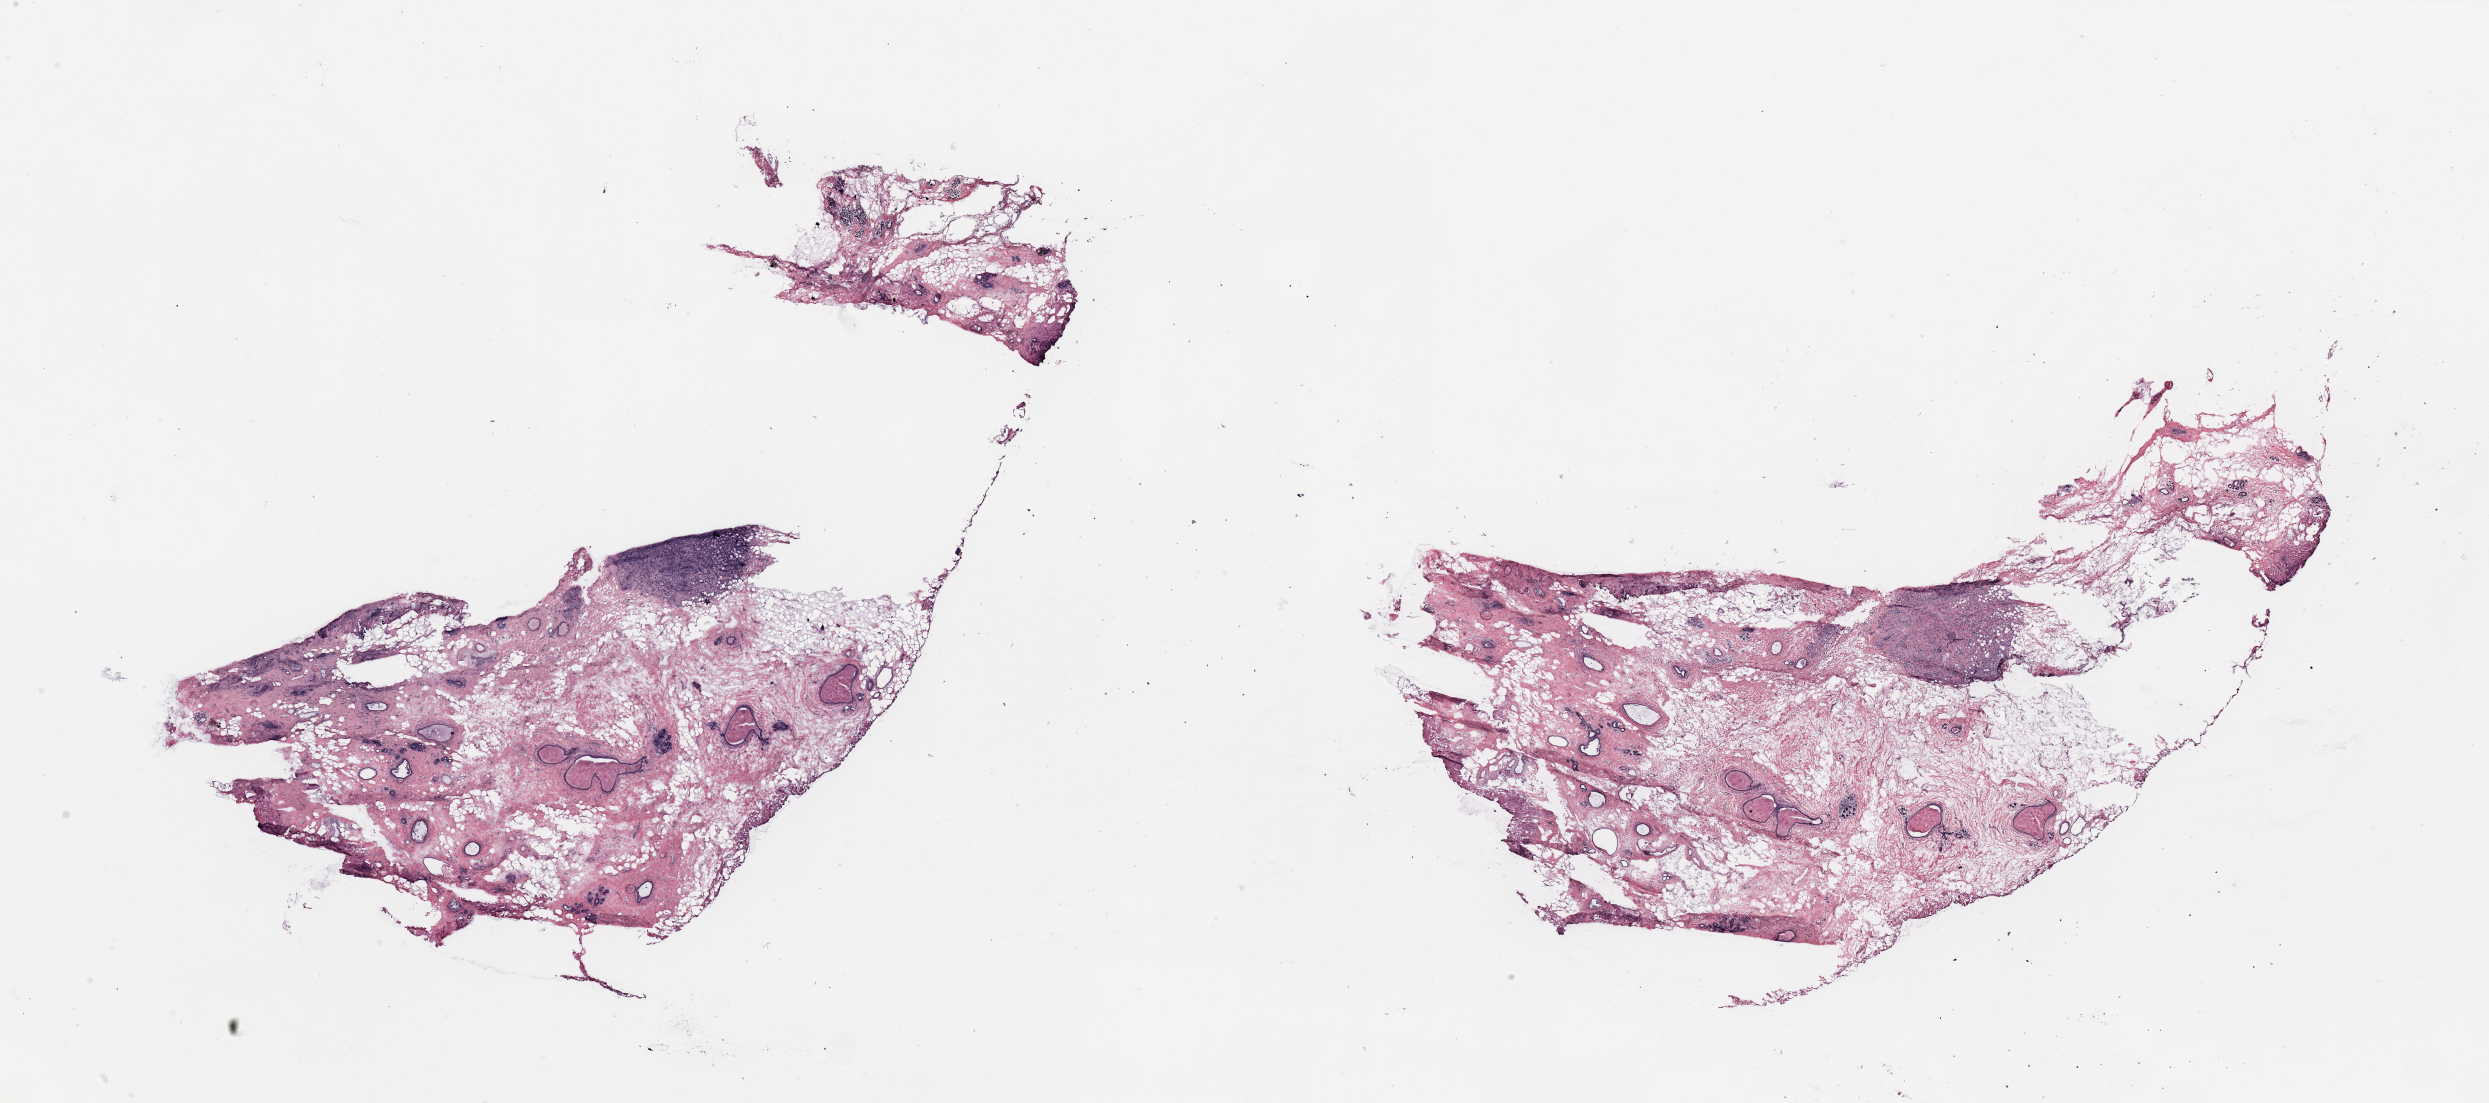
Whole-slide histology image, Hematoxylin and eosin (H&E) stained — shown as a low-resolution overview of the whole scanned area (about 39.4 x 17.5 mm, acquisition: 20x scan), tumour tissue sample, breast. Patient: female, age 54 years.
Diagnosis: Infiltrating lobular carcinoma, NOS.